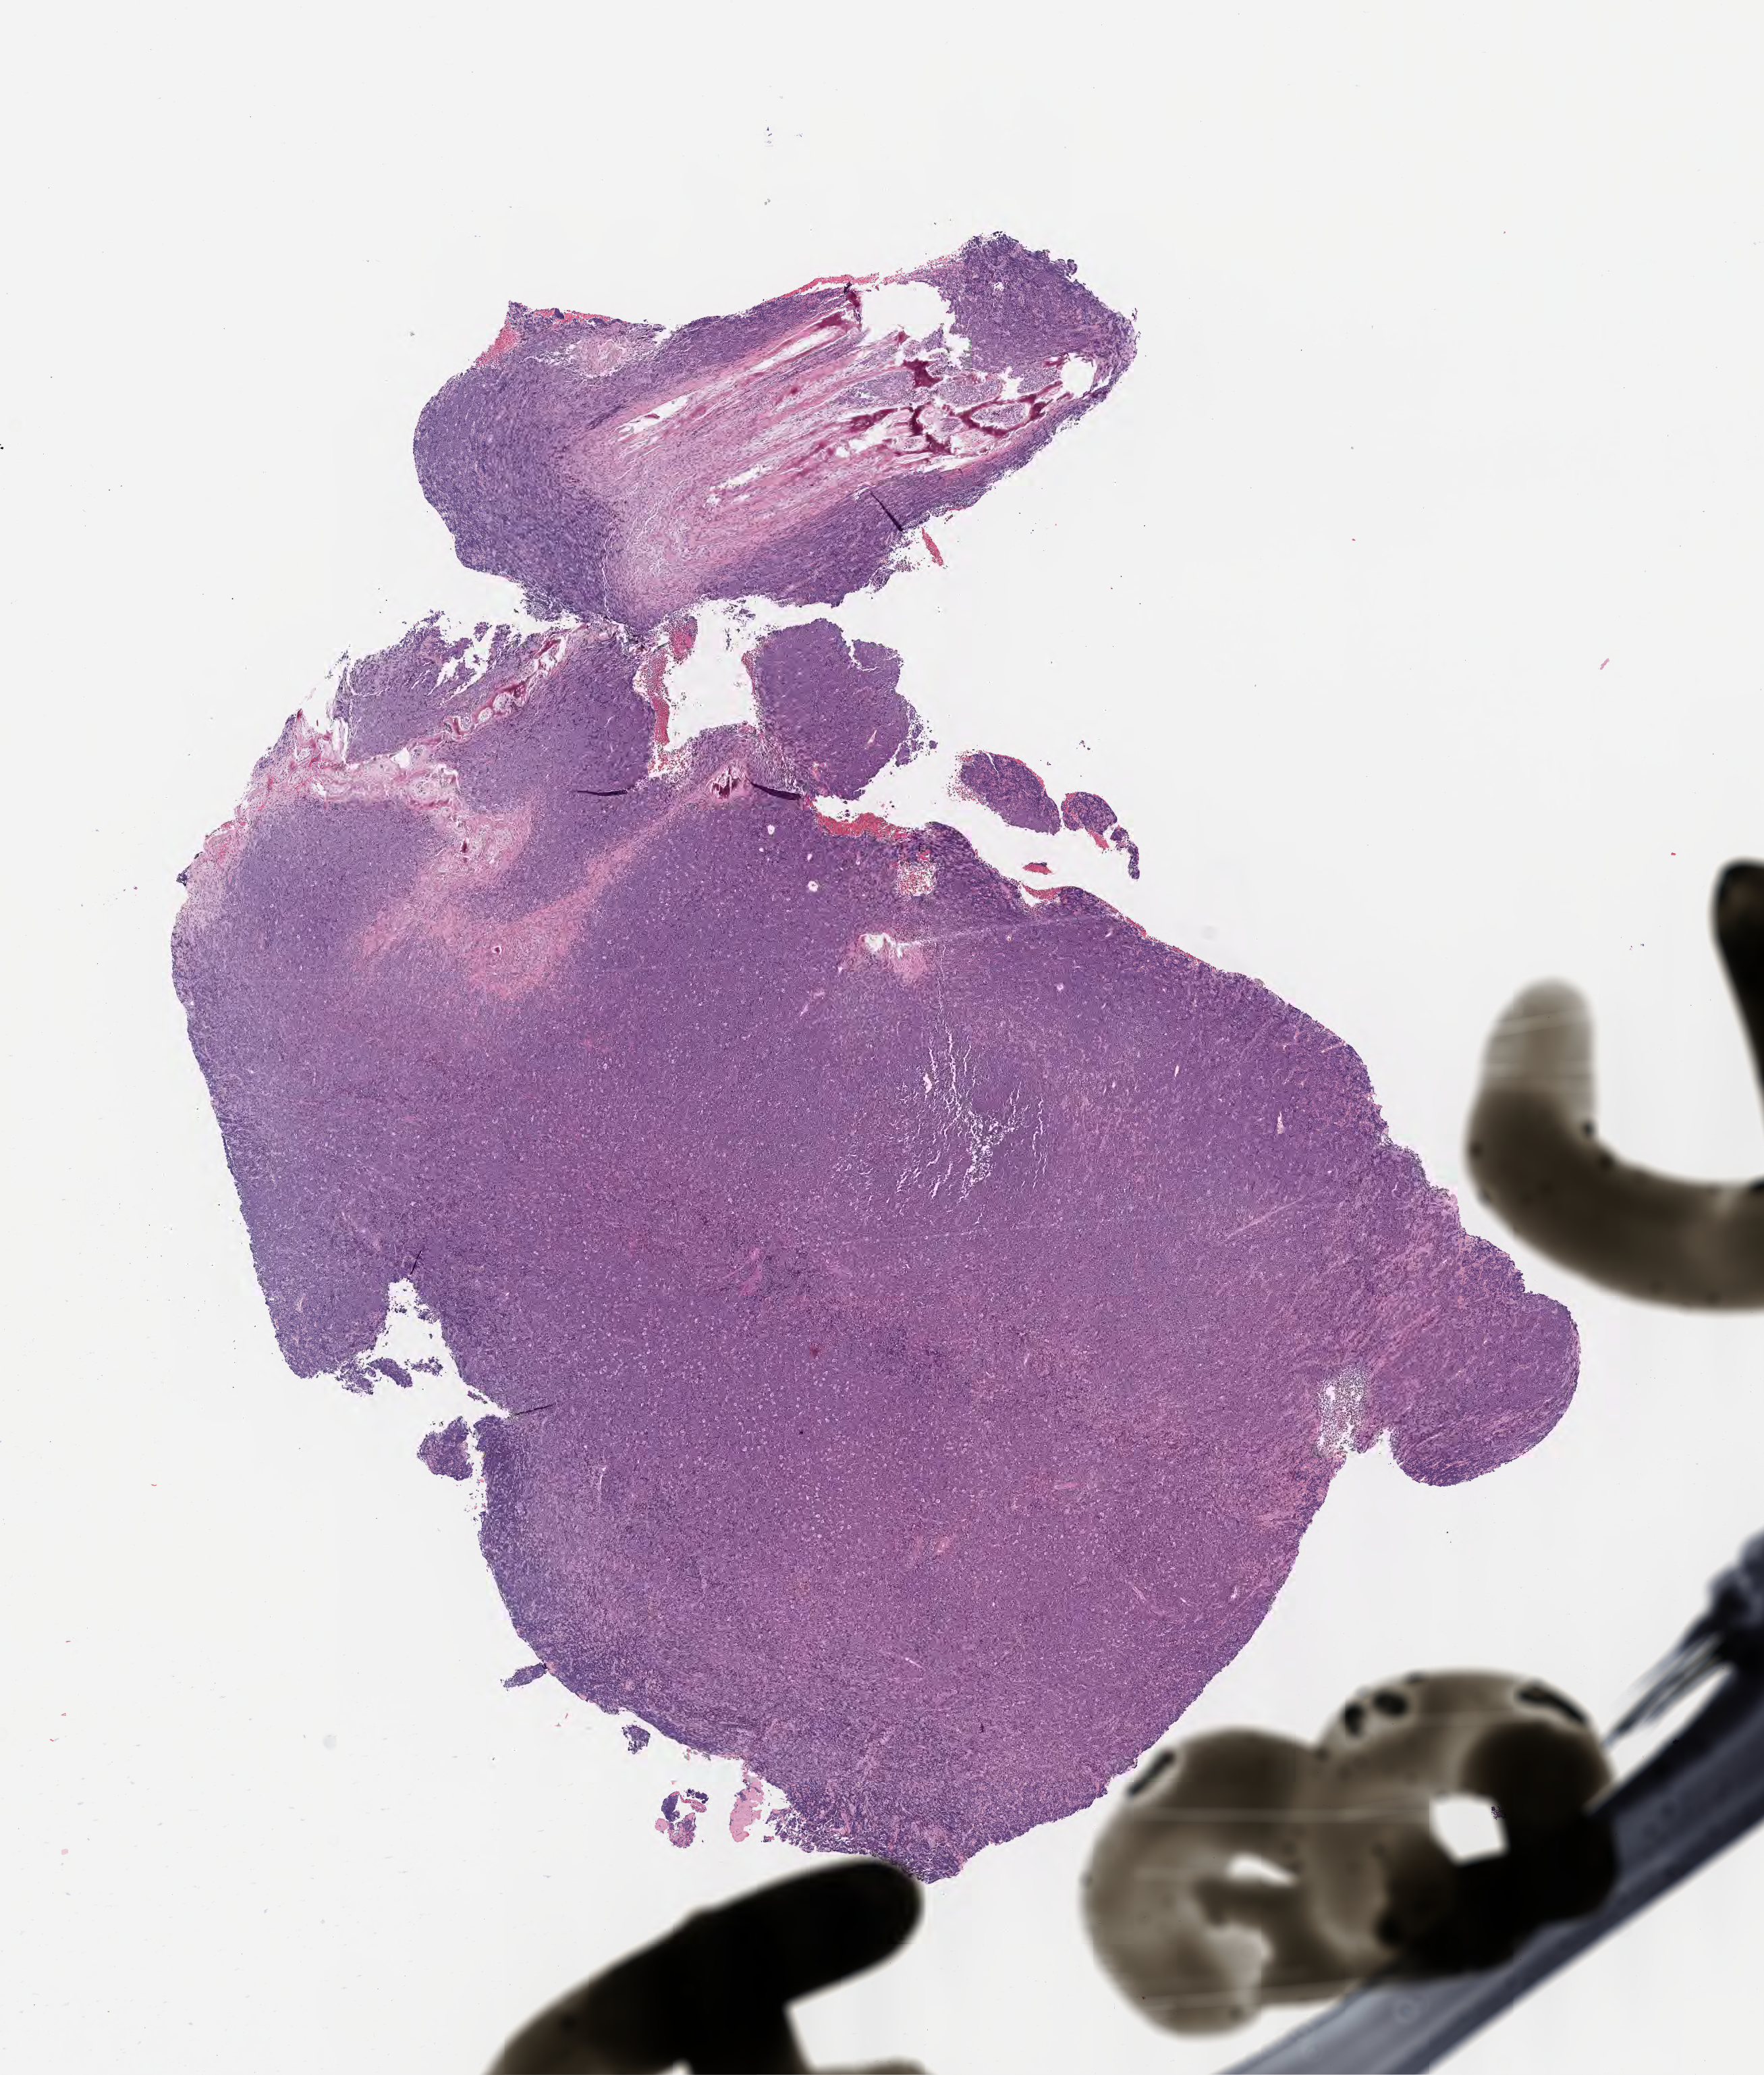
Digitized hematoxylin and eosin (H&E)-stained section, shown as a low-resolution overview of the whole scanned area (about 10.6 x 12.4 mm); specimen: tumor tissue; site: mandible. Patient: male, aged 19.
- diagnosis: Burkitt lymphoma, NOS